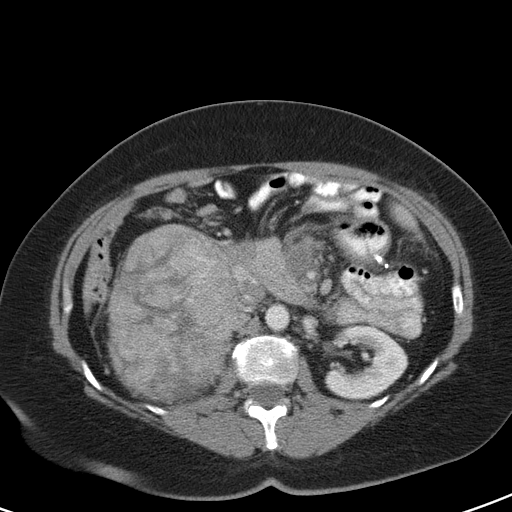
Contrast-enhanced abdominal CT, one axial slice; slice 63 of 126 in the series (ordered by position); 120 kVp; intravenous contrast given; soft-tissue window (W 400 / L 40 HU); 5 mm slice thickness; 512 × 512 image matrix. Patient: female, 51 years. From the clinical record (not read from this slice): diagnosis: adrenocortical carcinoma; tumour side: right adrenal; tumour size at pathology: 17 cm; Ki-67 index: 12 %; stage (as recorded): 2.
Outlined on this slice (semi-automatically segmented with operator editing):
- mass: bounding box (x1, y1, x2, y2) in pixels: (112, 225, 236, 404)